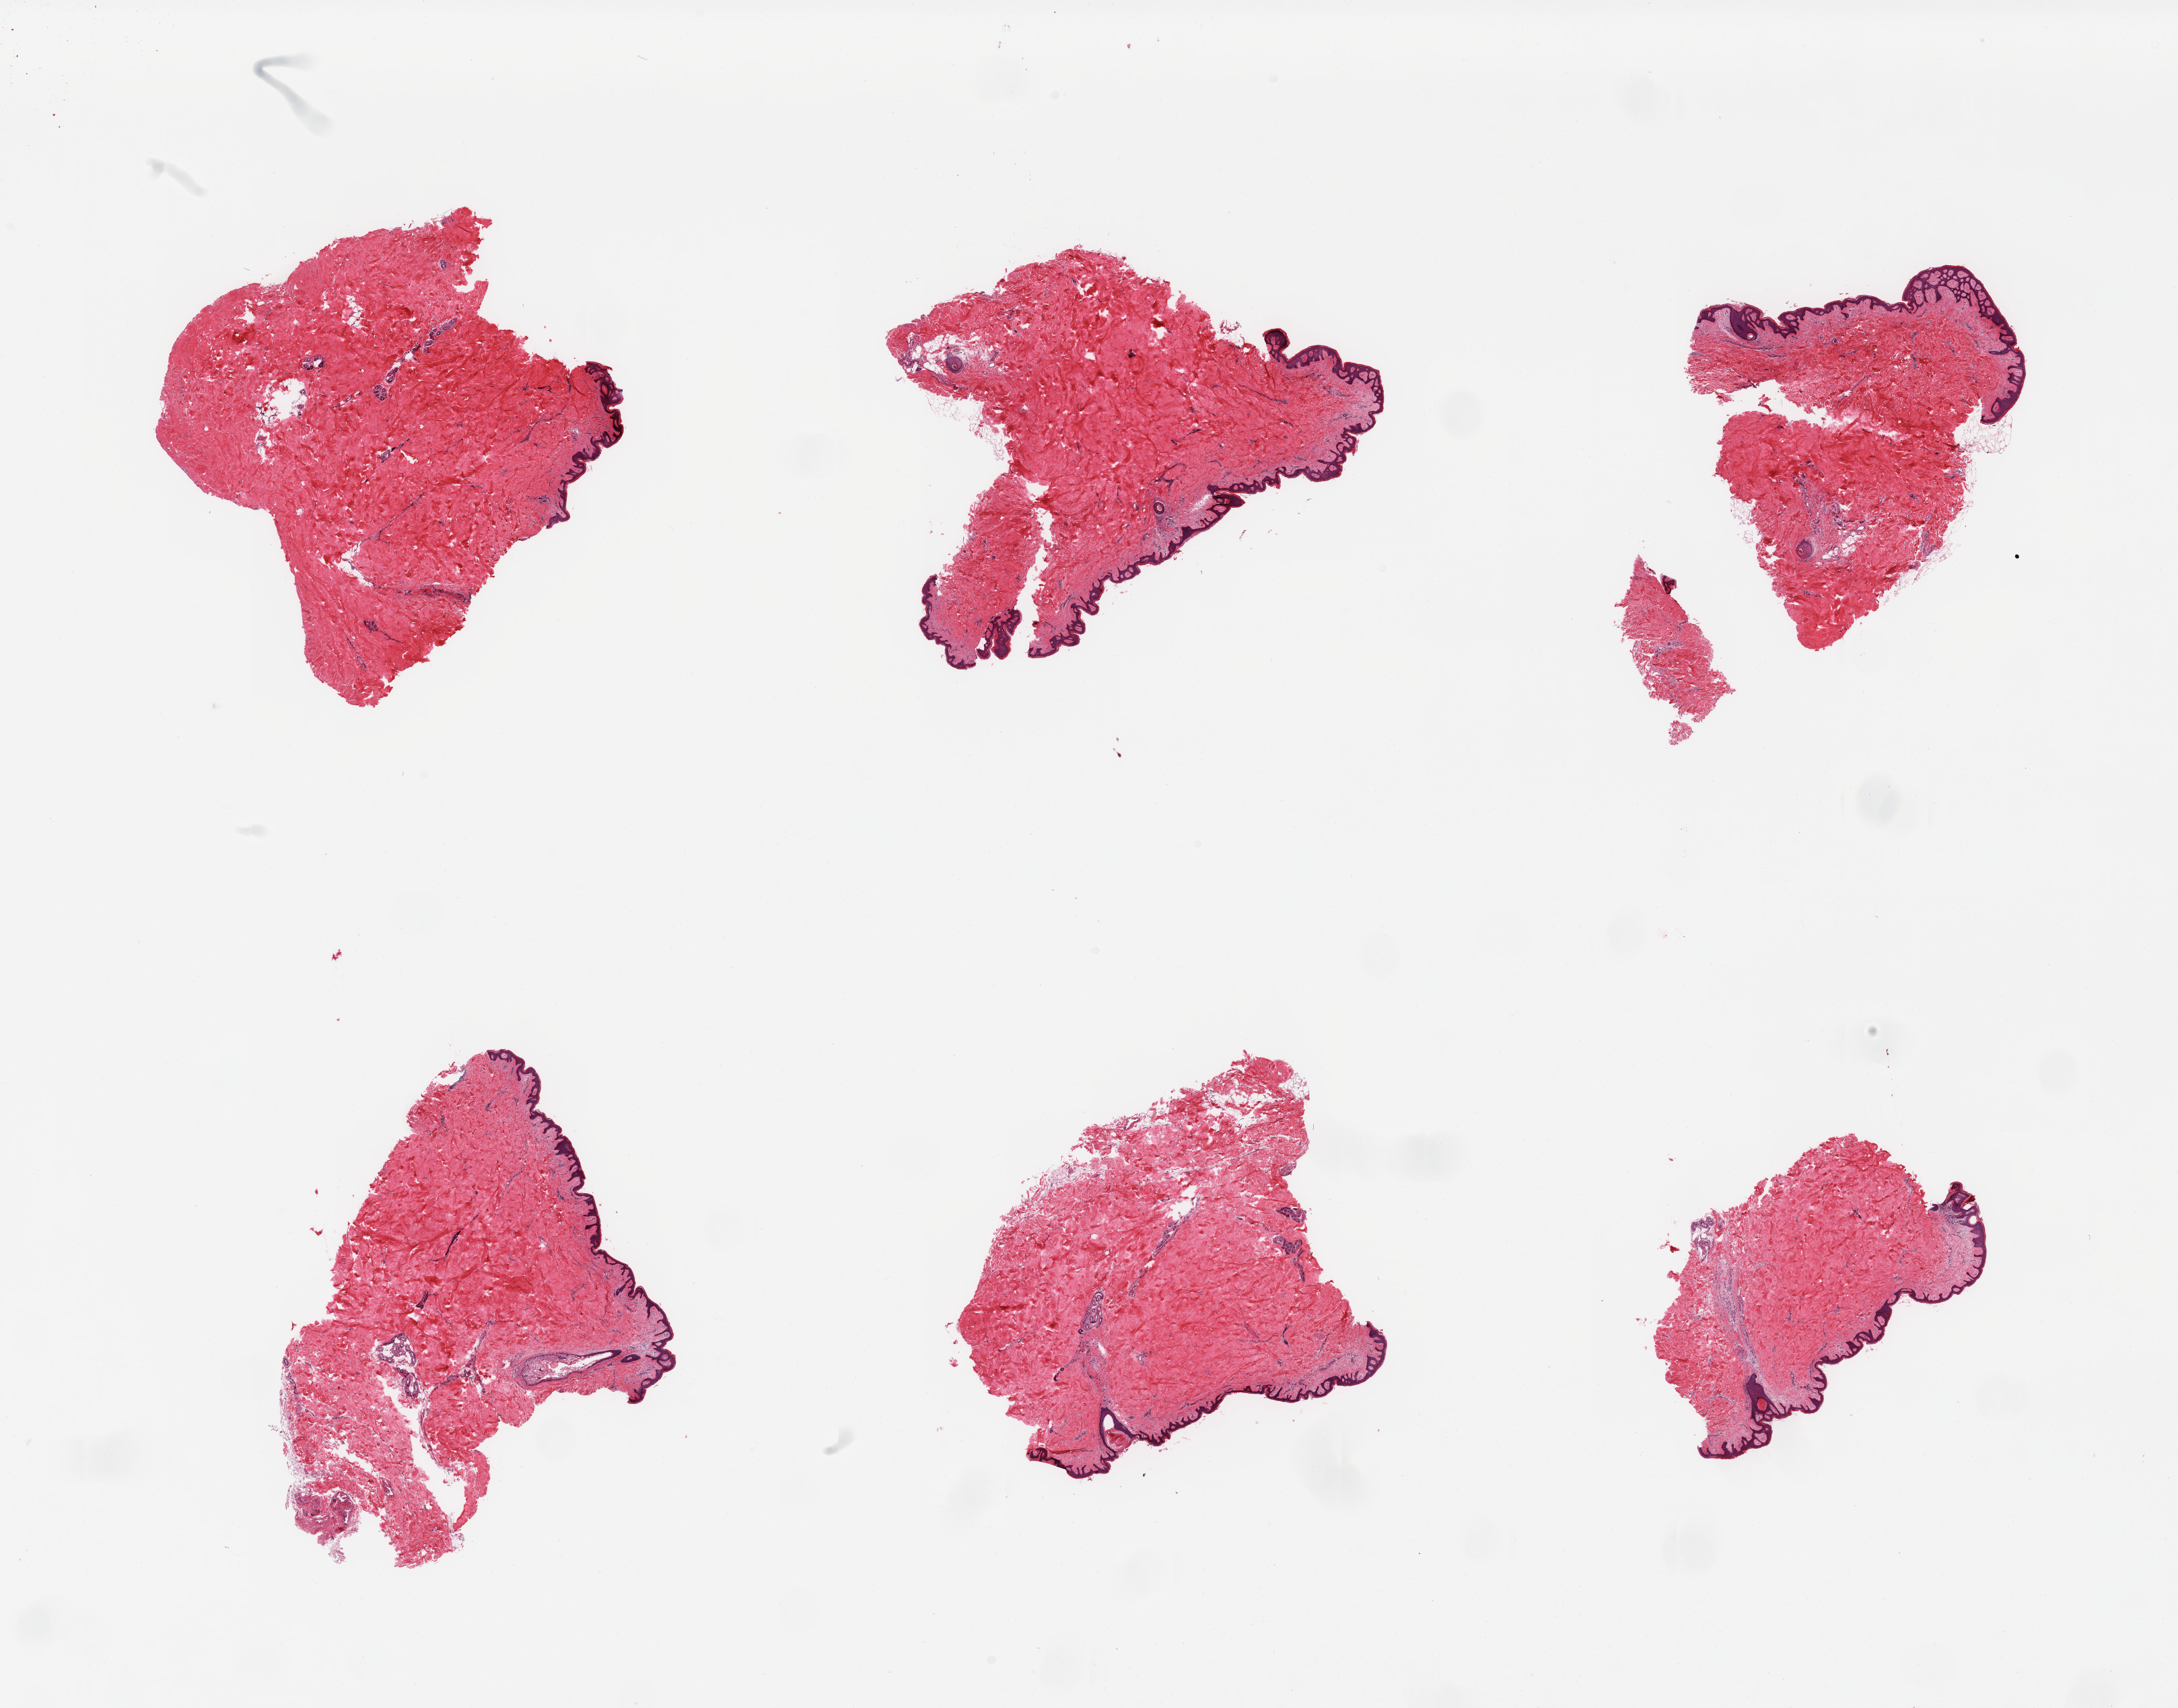
H&E whole-slide image, brightfield — a low-resolution overview of the entire scanned area, about 25.6 x 20.1 mm. PAXgene-fixed, paraffin-embedded tissue. Sampled site (target tissue): skin of suprapubic region. Tissue donor sample. Male donor.
* reviewer comment on this tissue sample: 6 pieces; well trimmed